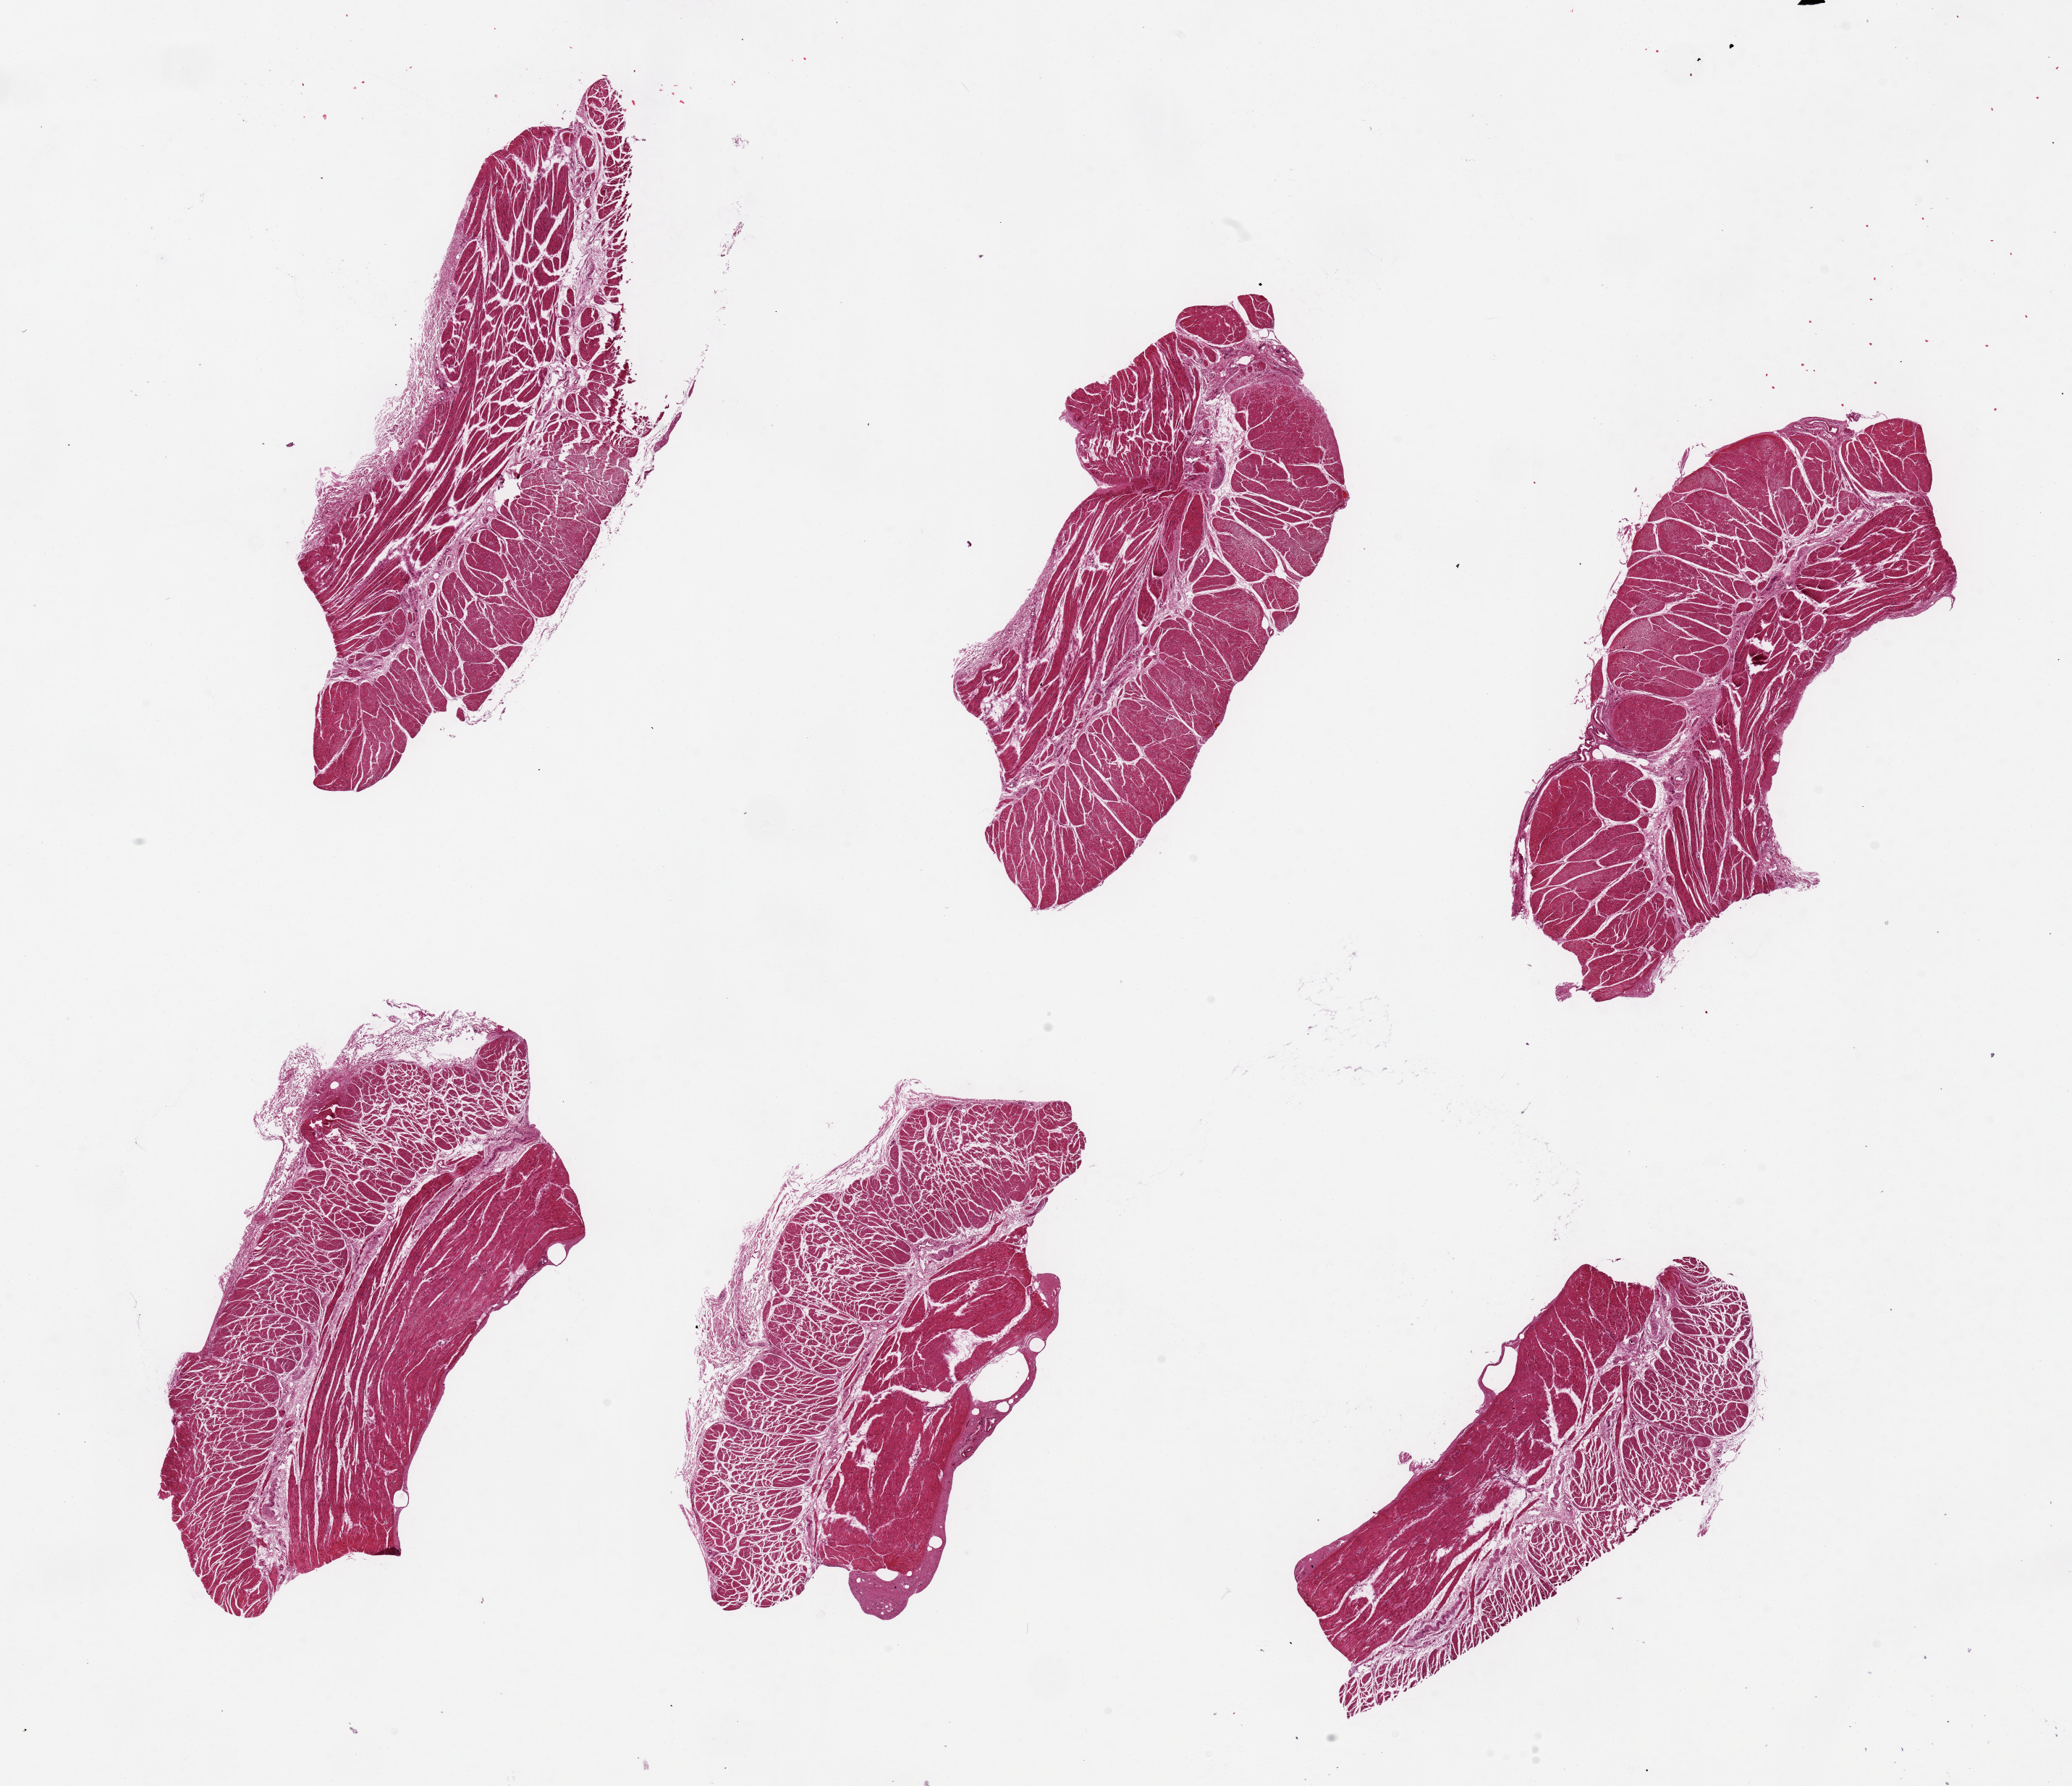
Hematoxylin and eosin (H&E) whole-slide image, low-resolution overview of the scanned area, about 22.6 x 19.5 mm (from a 20x scan). PAXgene-fixed paraffin-embedded (PFPE) section. Target tissue: esophageal muscle. Tissue donor sample. Female donor.
Reviewer comment on this tissue sample: 6 pieces, ~ 7x2.5mm.